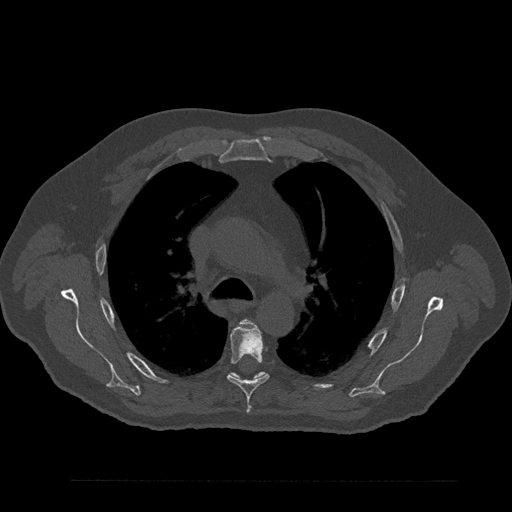
CT including the spine, one axial slice. Slice 598 of 797 in the series (ordered by position). Reconstruction kernel Br40s/3. Bone window (W 1800 / L 400 HU). 0.5 mm slice thickness. 512 × 512 image matrix, field of view 430 × 430 mm. Male patient, age 61 years. From the clinical record (not read from this slice): primary cancer: prostate.
Outlined on this slice (semi-automatic segmentation, software-assisted and operator-edited):
- T4 vertebra: bounding box <242,320,250,323> (left, top, right, bottom; pixels)
- T5 vertebra: <227,325,269,408>
- T6 vertebra: <228,372,267,382>